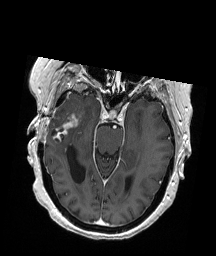
Brain MRI from a brain-tumour surgery series, one axial slice; T1-weighted post-contrast; 1 mm slice thickness; 216 × 256 image matrix, field of view 211 × 250 mm. From the clinical record (not read from this slice): histopathology: Glioblastoma; WHO grade: 4; IDH mutation: no.
Structures marked on this image (expert manual segmentation):
- tumour: box from (x=55, y=115) to (x=80, y=138) px